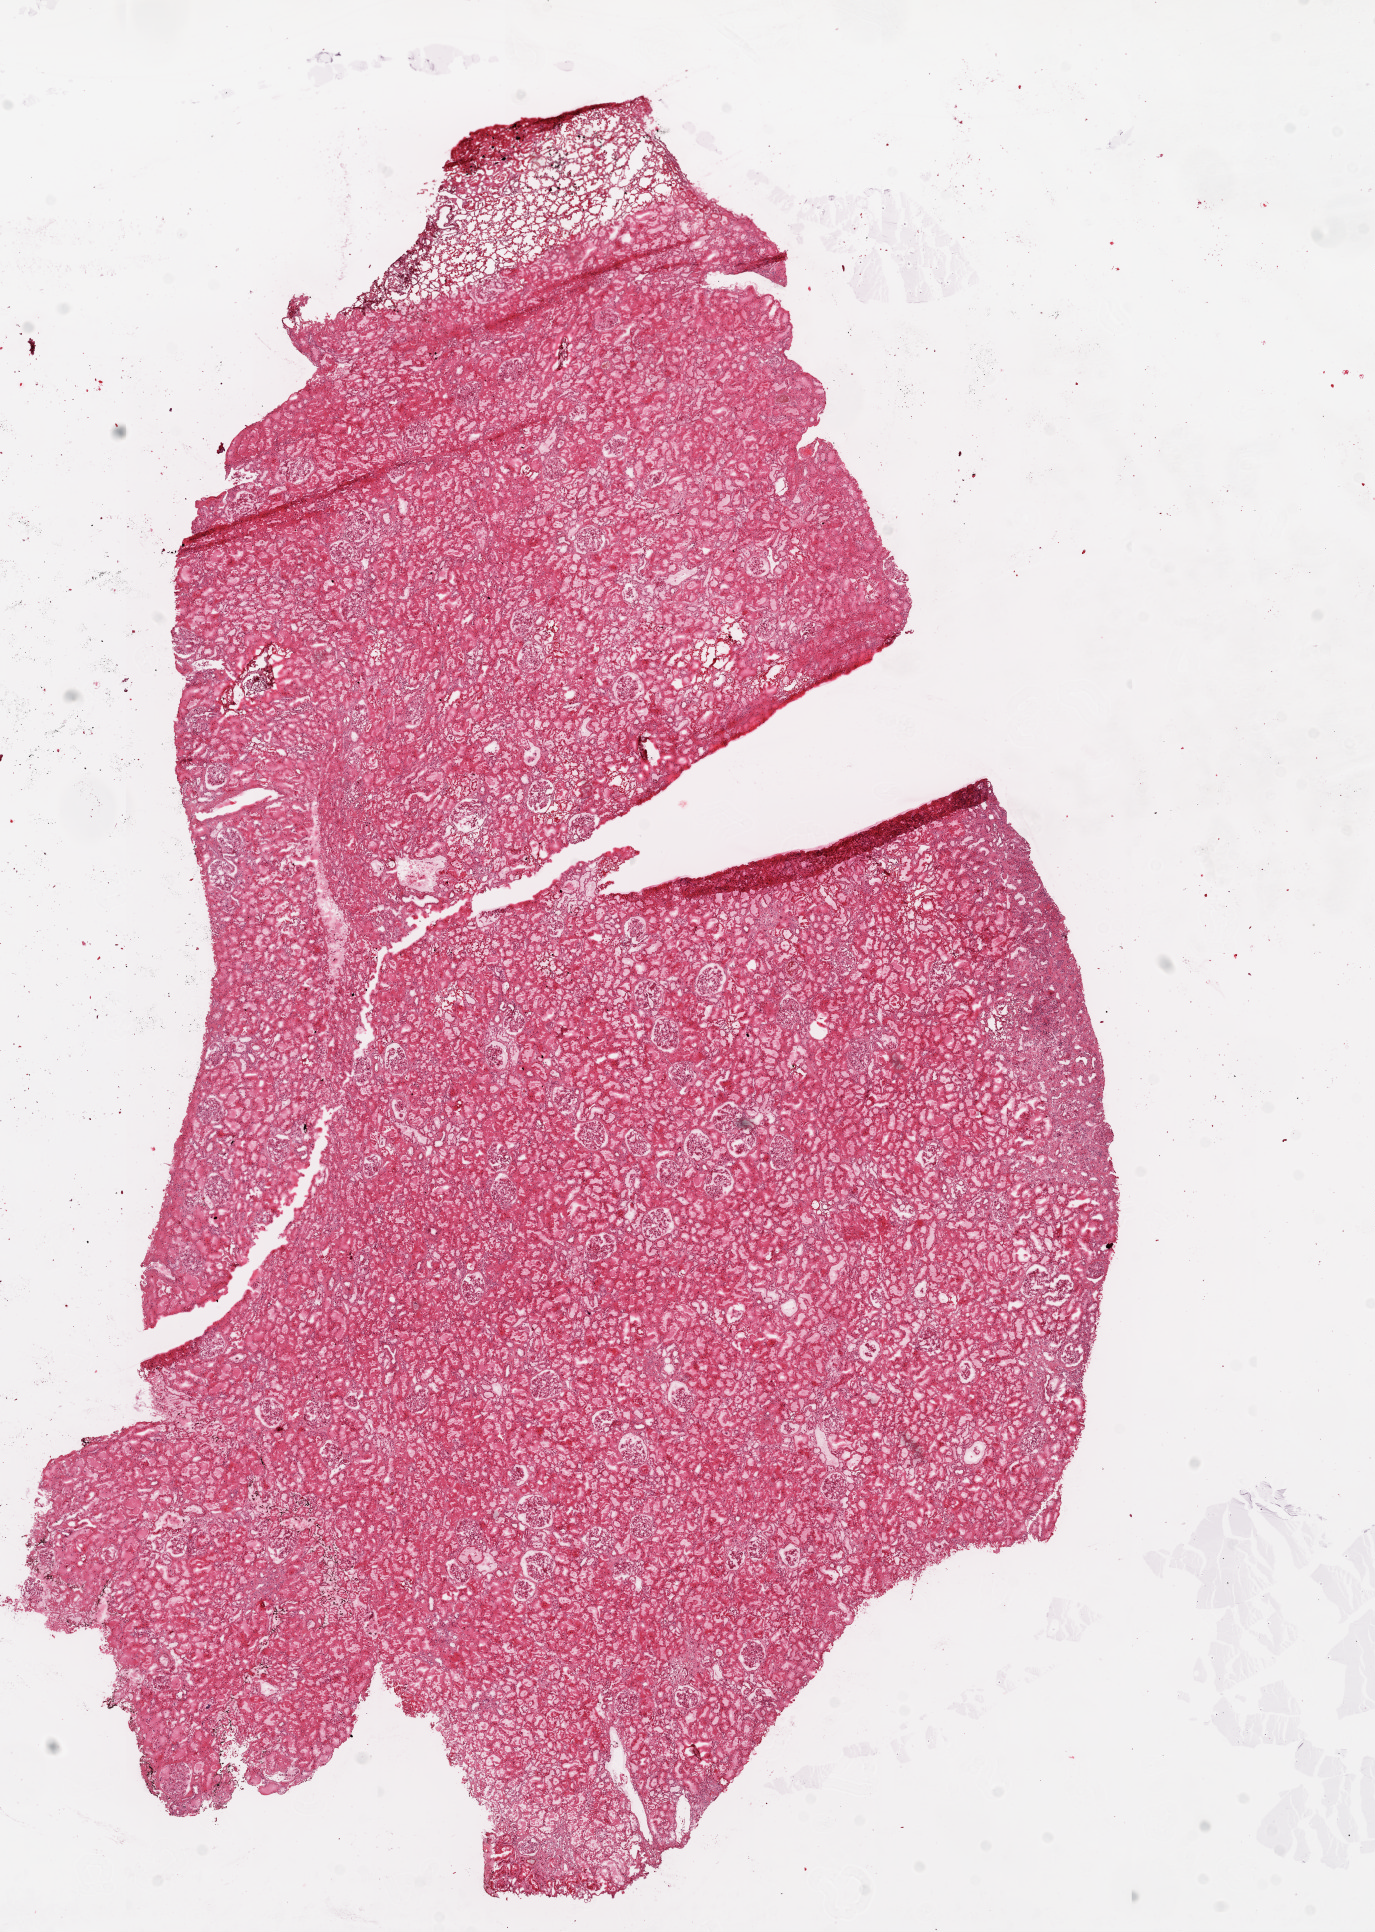
H&E whole-slide image — whole scanned area (about 11.0 x 15.5 mm, from a 20x scan) shown as a low-resolution overview. Frozen section from the top of the tissue portion. Solid tissue normal (non-tumour tissue) sample from the kidney. Patient: male, age at initial diagnosis 49 years.
This section: solid tissue normal (non-tumour) sample from the same patient. Patient diagnosis: Clear cell adenocarcinoma, NOS.